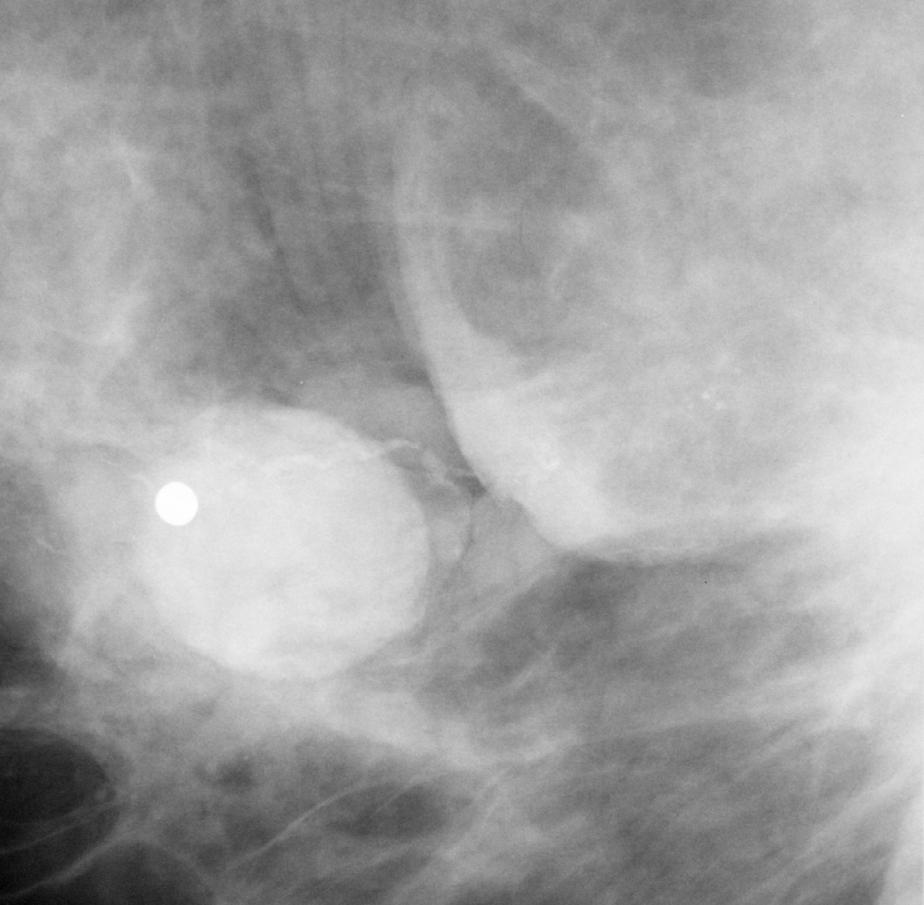
Crop from a digitized film mammogram around one marked abnormality; right breast; MLO view; BI-RADS breast density category 2 (scale 1–4).
Finding: calcifications, morphology pleomorphic / fine linear branching, distribution clustered / linear; BI-RADS assessment category 5; subtlety rating 5 on a 1 (subtle) to 5 (obvious) scale; pathology result (as recorded, not read from the image): malignant.